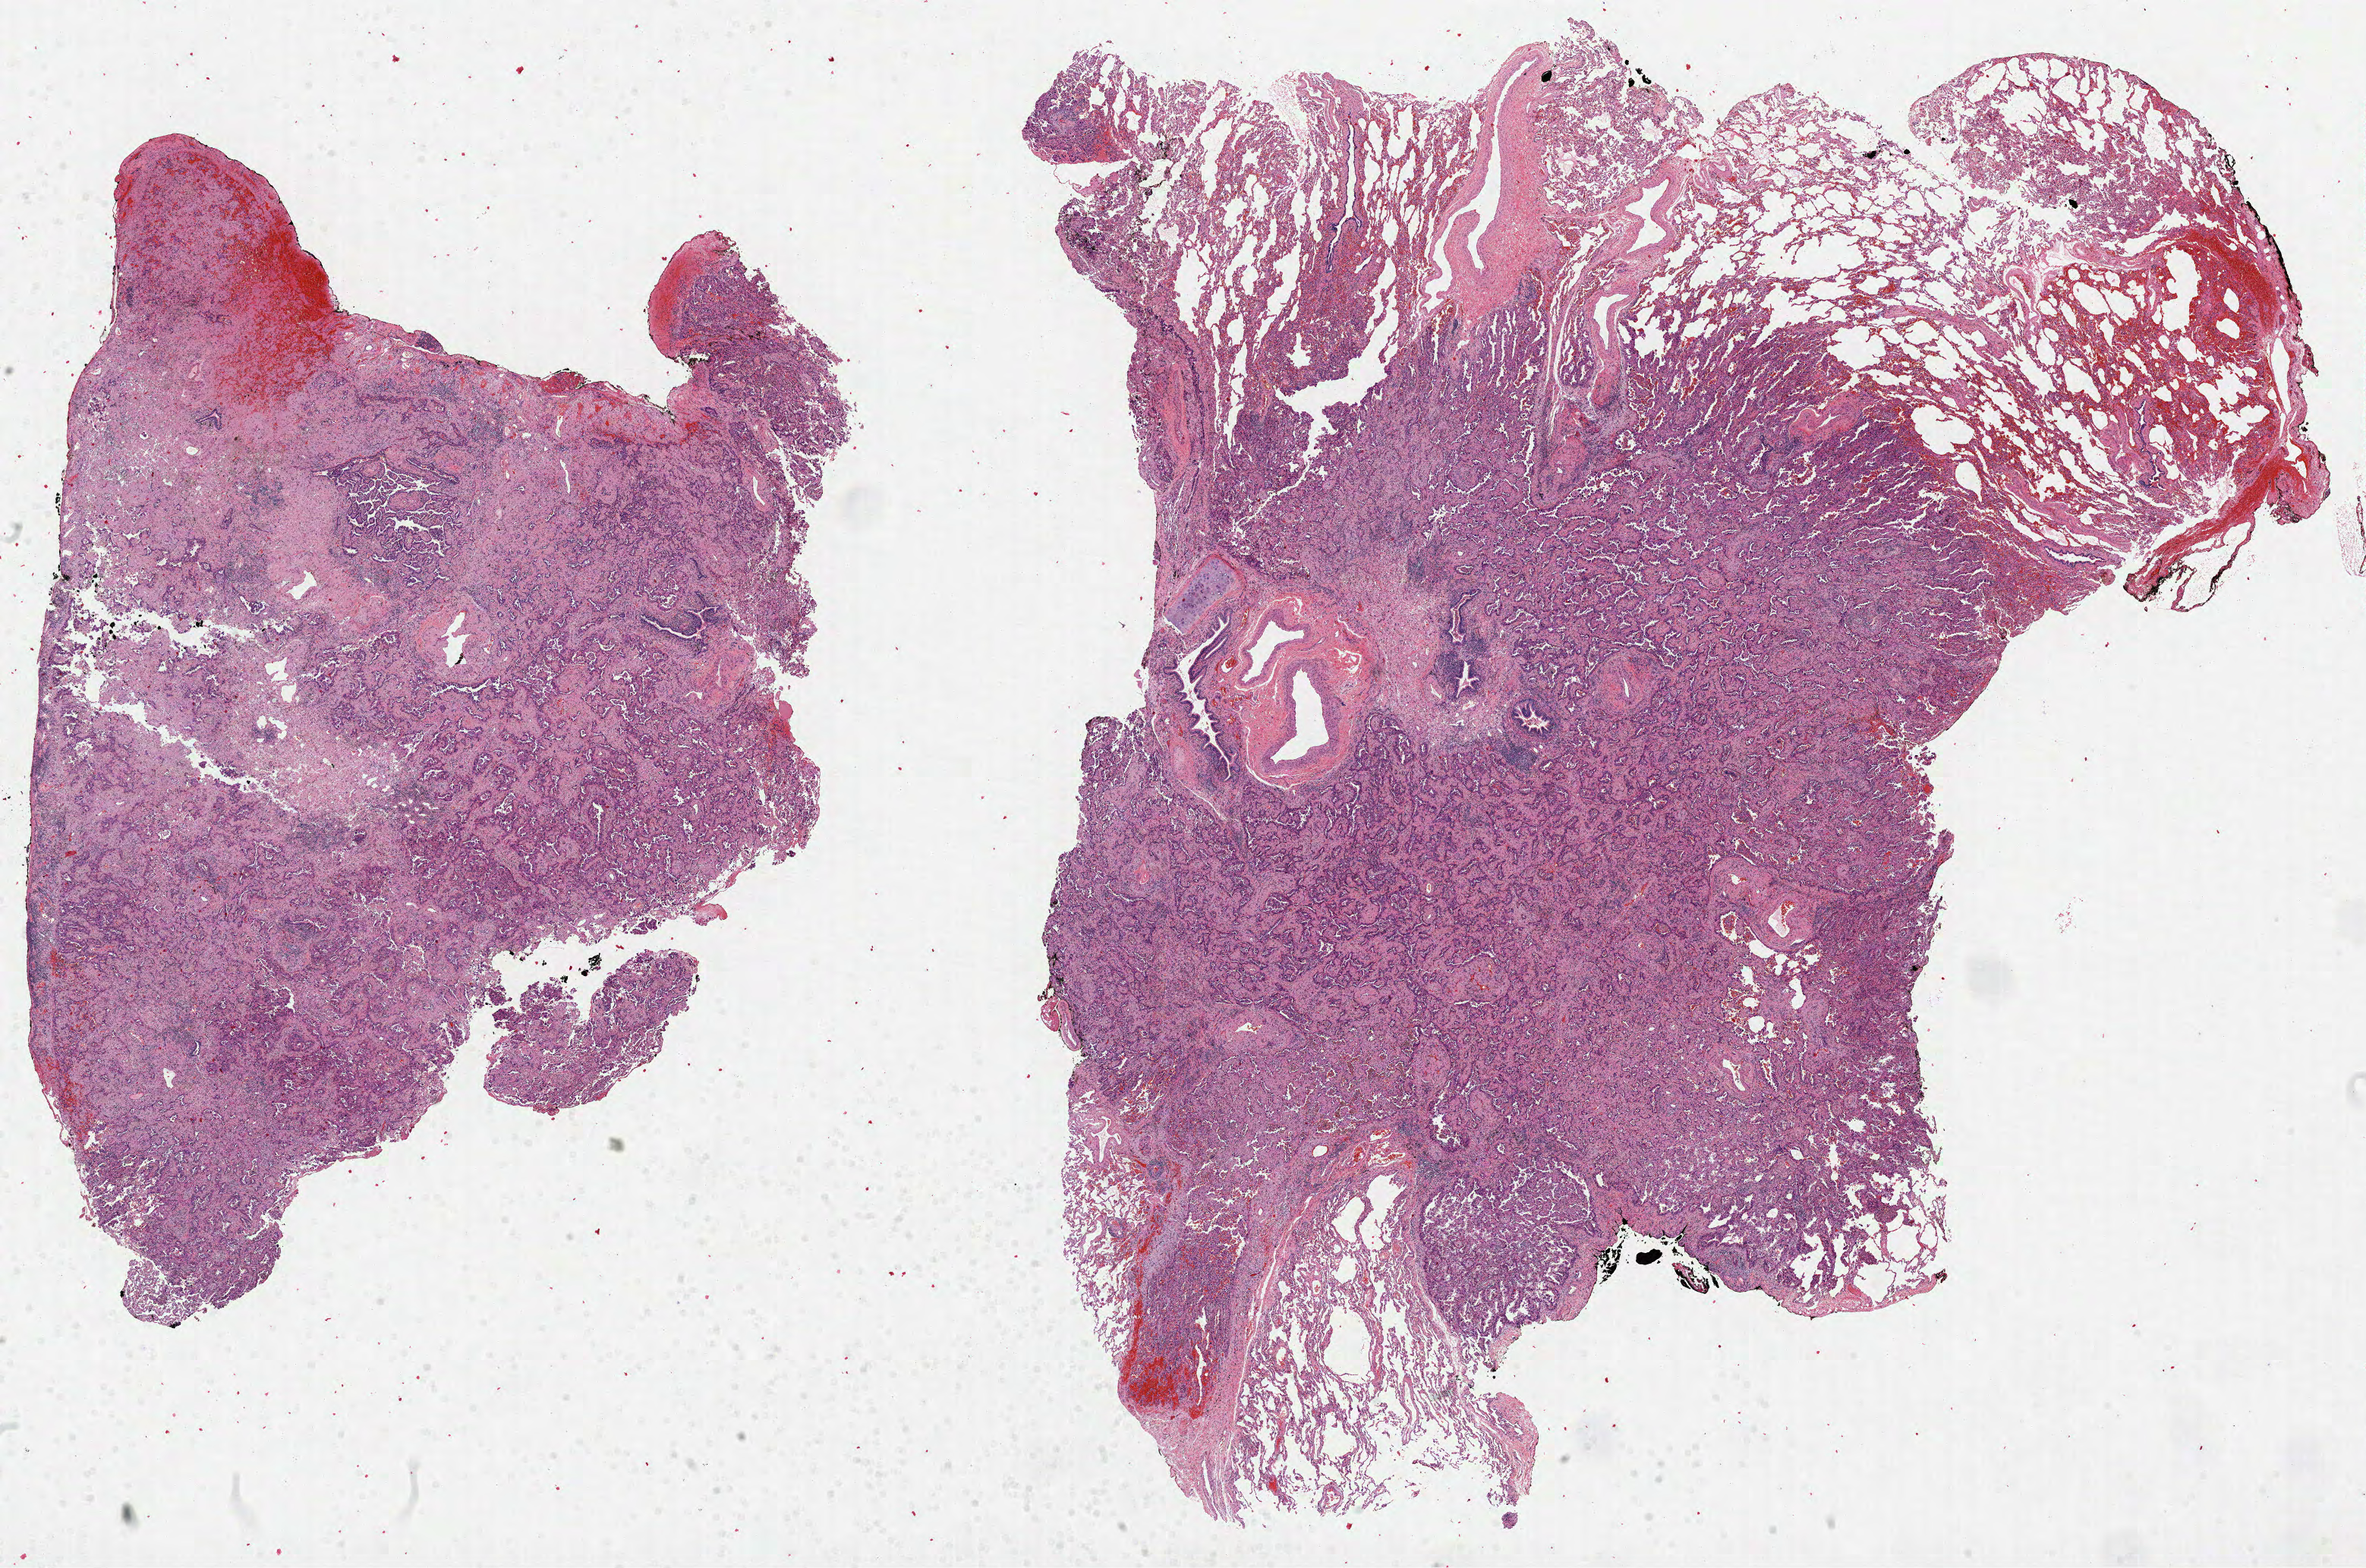
H&E whole-slide image, low-resolution overview of the scanned area, about 25.1 x 16.7 mm (from a 40x scan). FFPE section. Sample: primary tumour, lung. Male patient; age at initial diagnosis 56 years.
Histologic diagnosis: Bronchiolo-alveolar carcinoma, non-mucinous.